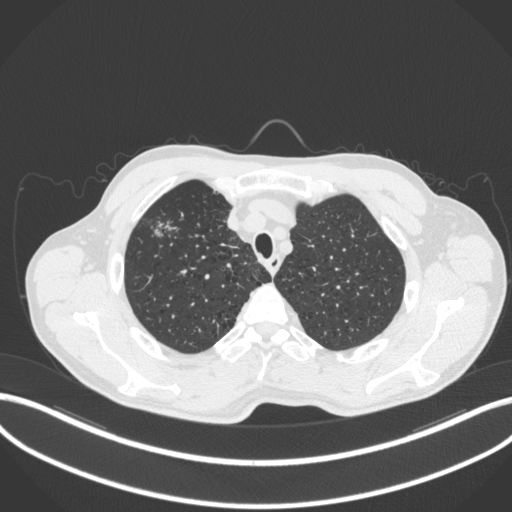
Chest CT, one axial slice. Slice 351 of 414 in the series (ordered by position). Reconstruction kernel B31f. 120 kVp. Lung window (W 1500 / L -600 HU). 512 × 512 image matrix, field of view 400 × 400 mm. Patient: male, 69 years. From the clinical record (not read from this slice): clinical TNM (as recorded): T1b N1 M0.
Annotated regions visible in this slice (rectangle marked by the reading radiologist):
- lung tumour (recorded histology: adenocarcinoma): box from (x=150, y=217) to (x=183, y=242) px